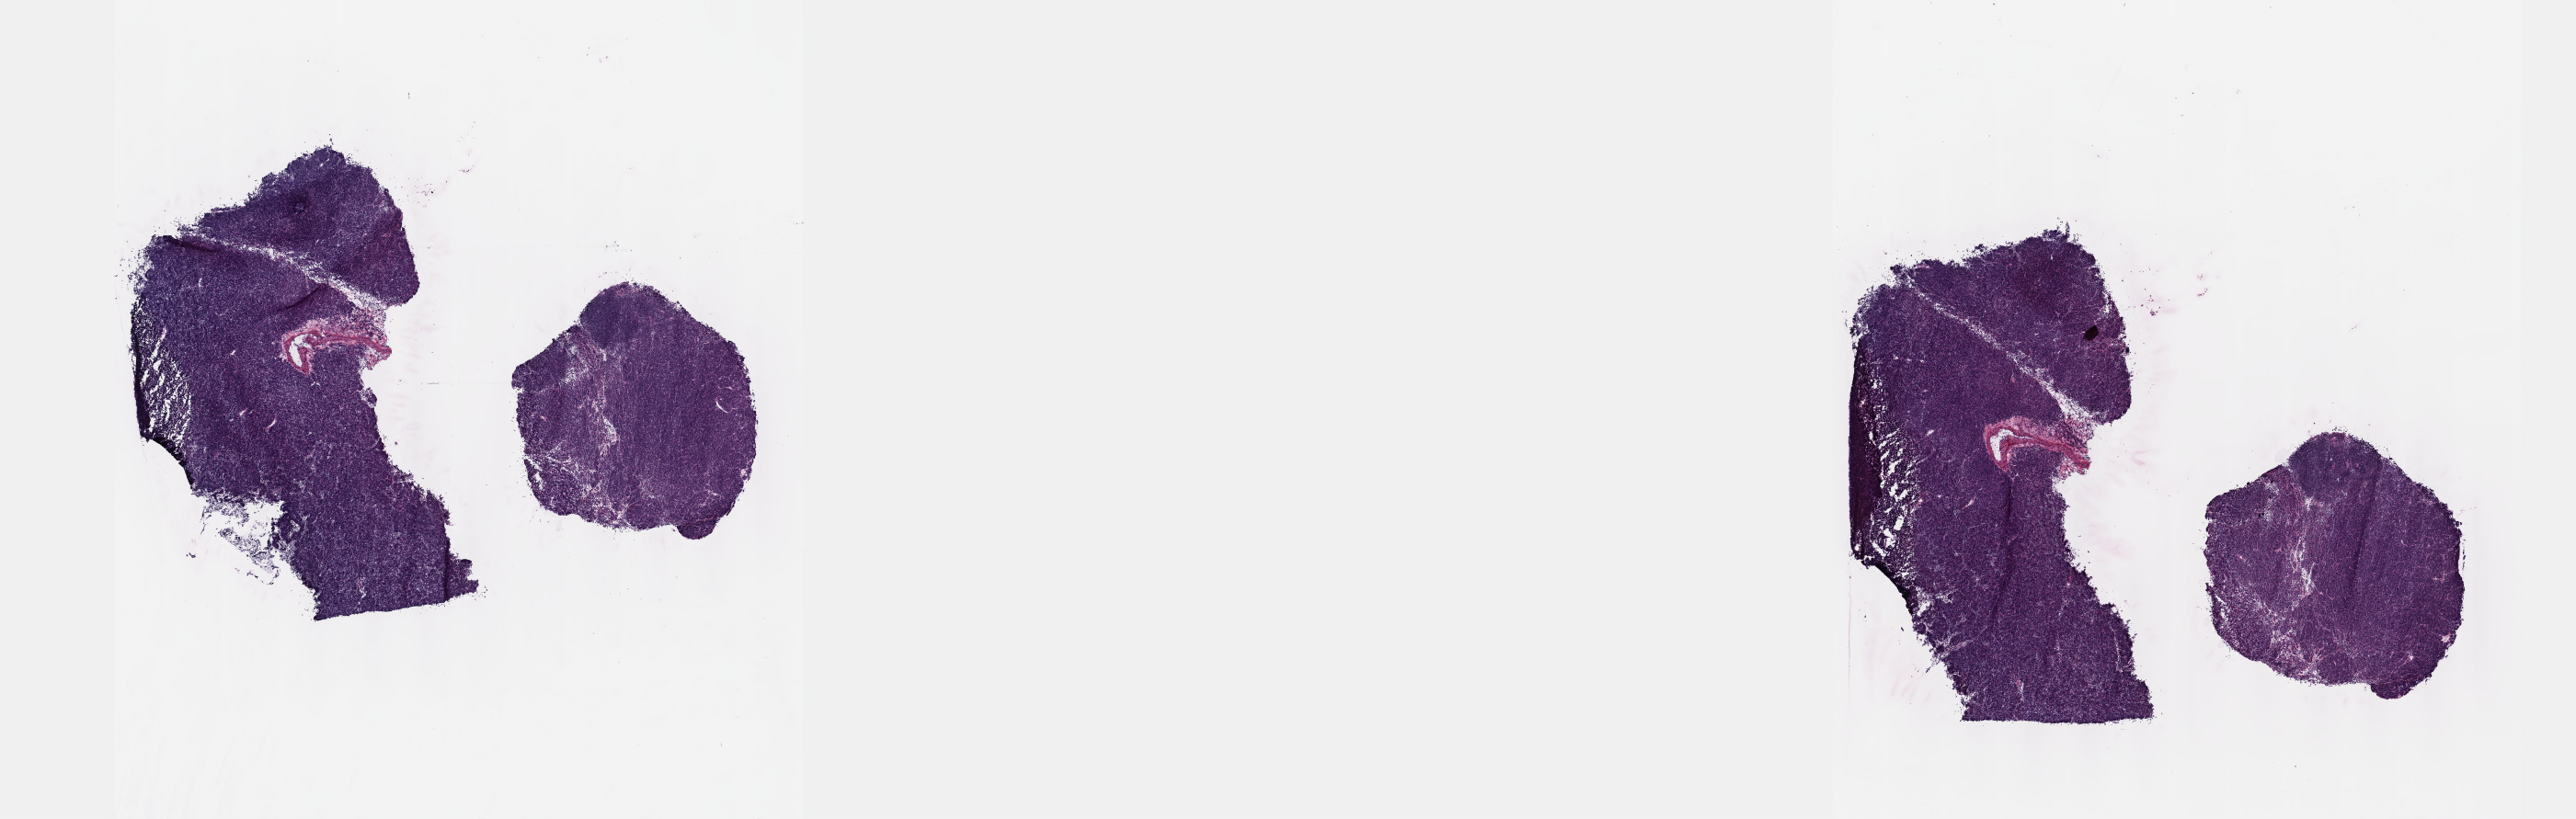
Whole-slide histology image, Hematoxylin and eosin (H&E) stained, shown as a low-resolution overview of the whole scanned area (about 22.6 x 7.2 mm), frozen section from the top of the tissue portion, thymus, primary tumour sample. Patient: male, age at initial diagnosis 40 years. Pathologist review of this section (percent, as recorded): tumour cells 99%, tumour nuclei 99%, normal cells 0%, stromal cells 1%, necrosis 0%. Infiltration values recorded for this section: lymphocyte infiltration 0%, monocyte infiltration 0%, neutrophil infiltration 0%.
Diagnosis: Thymoma, type AB, malignant.